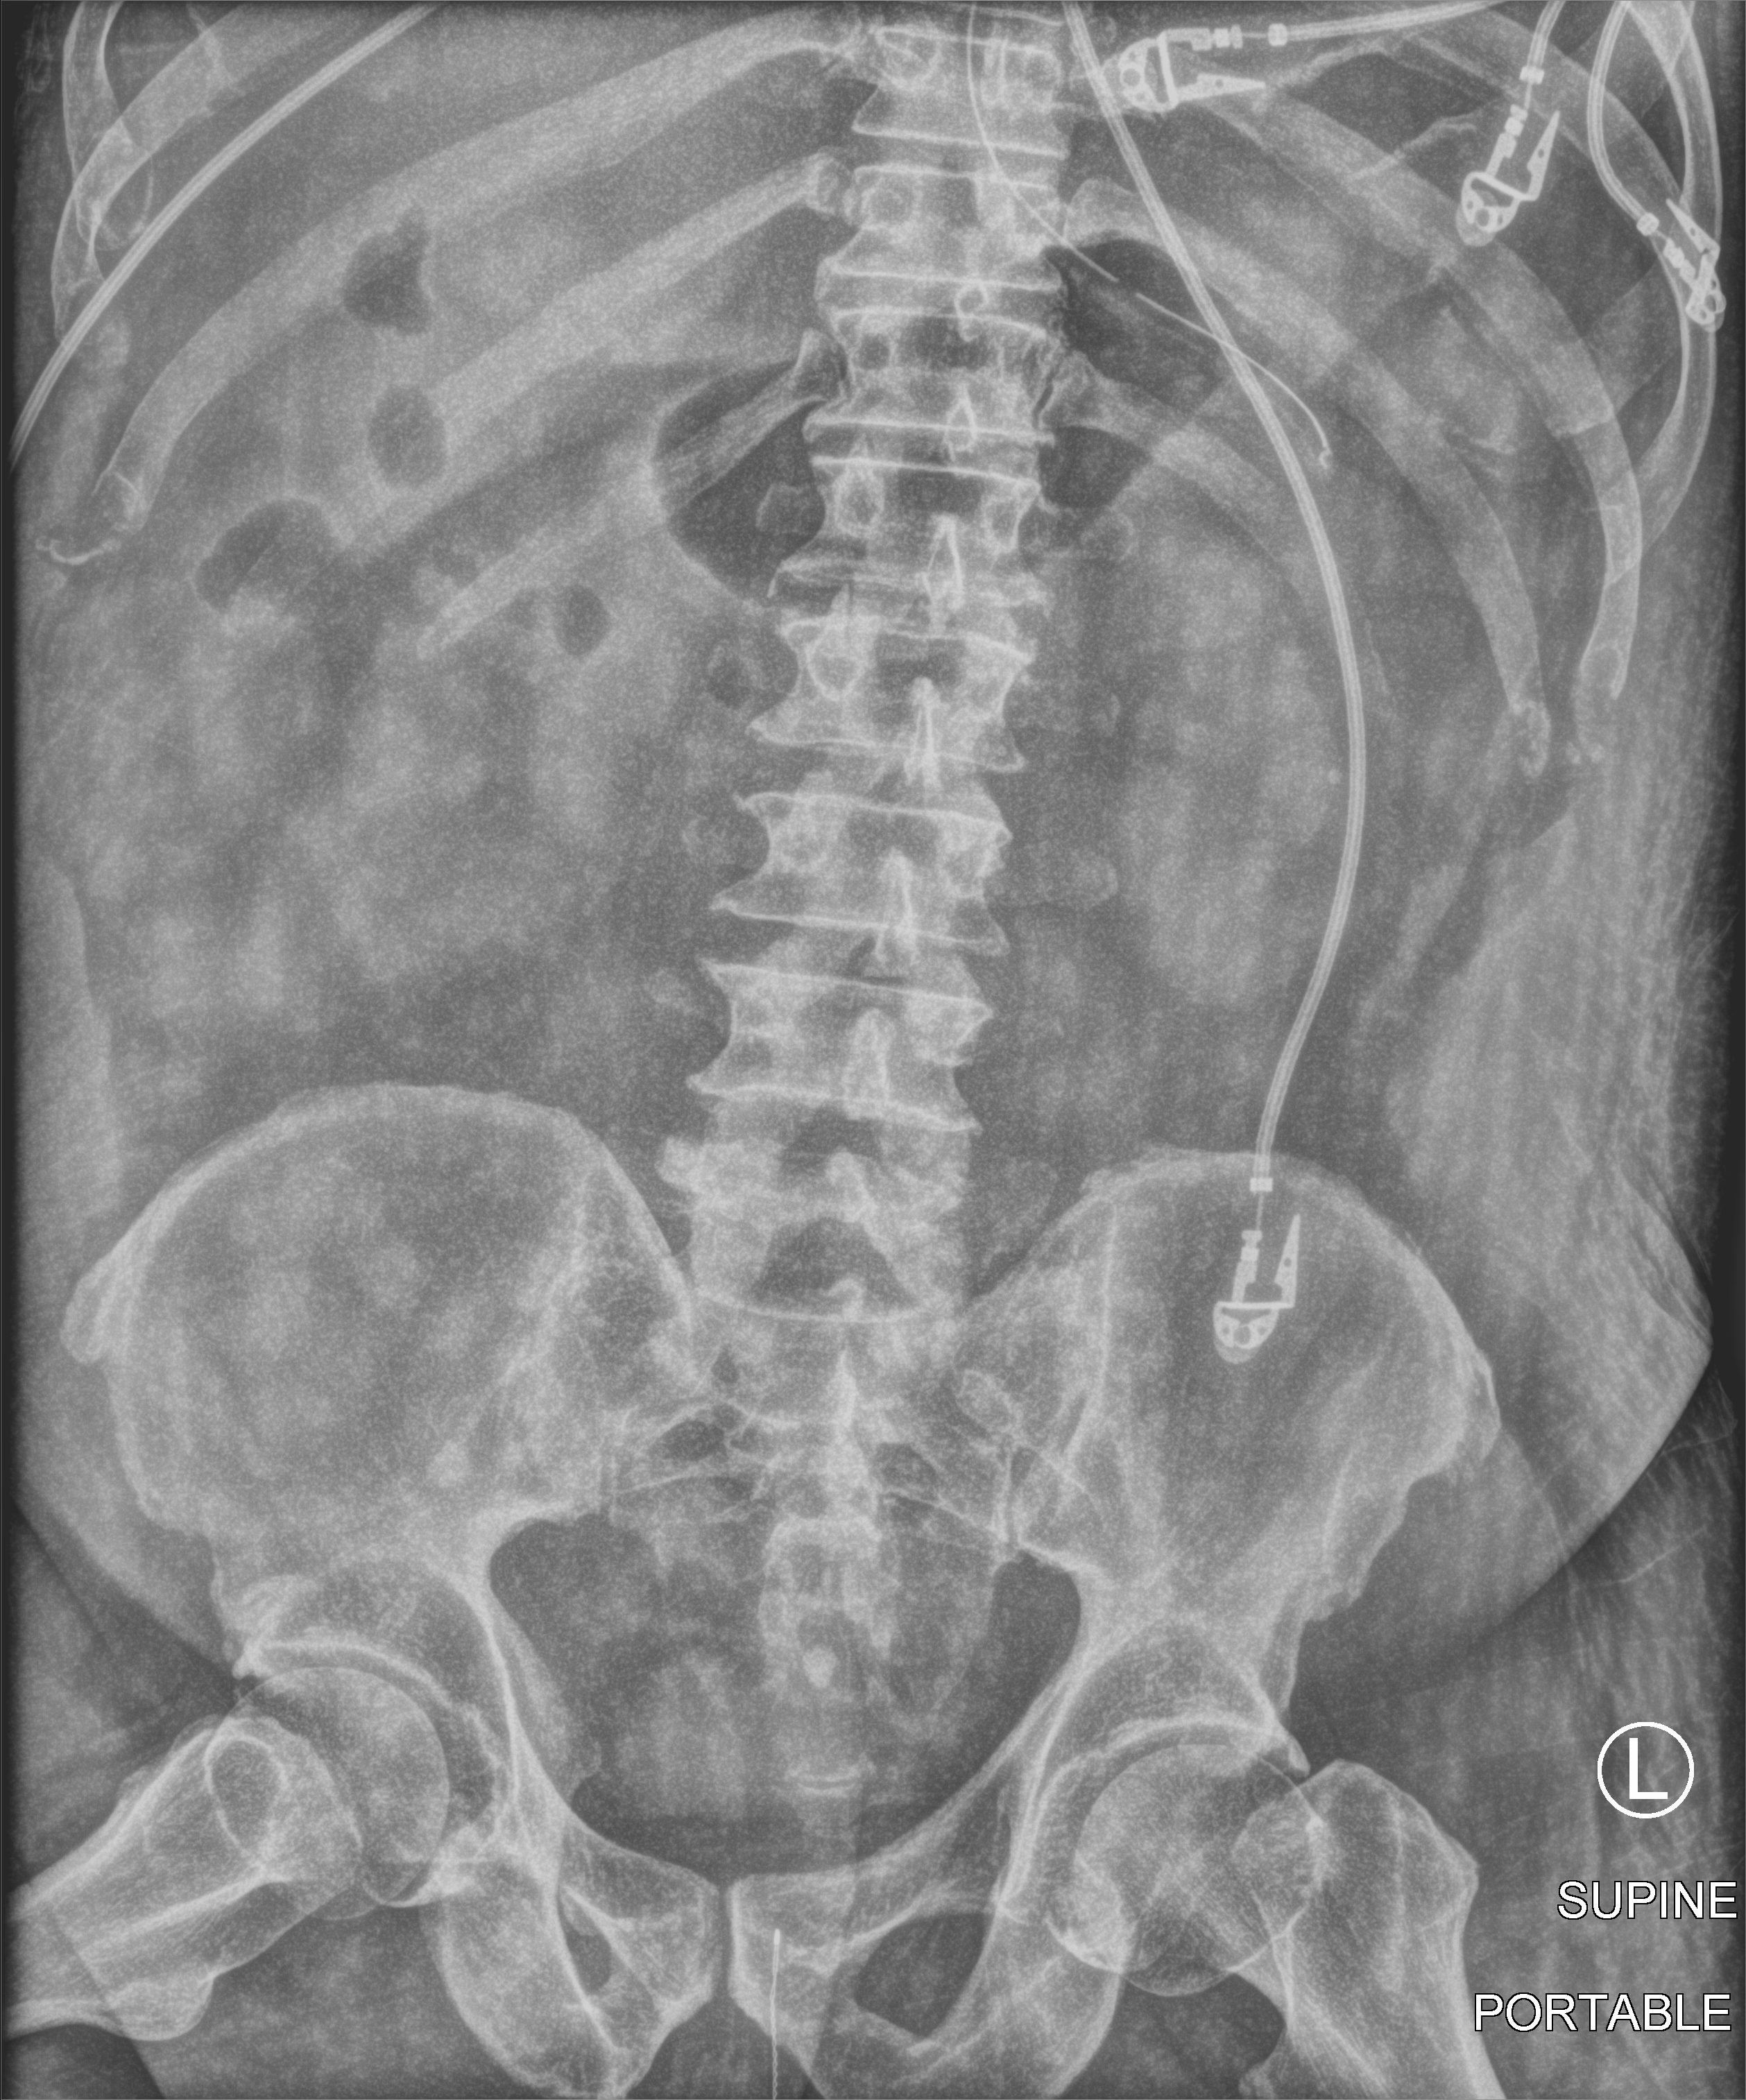
Bedside abdomen radiograph (computed radiography). Patient hospitalised with COVID-19; male, aged 60–74 years.
From the hospital-stay record, not from the radiograph (when in the stay this image was taken is not recorded):
- diabetes (admission record): no
- mechanically ventilated during this hospital stay: yes